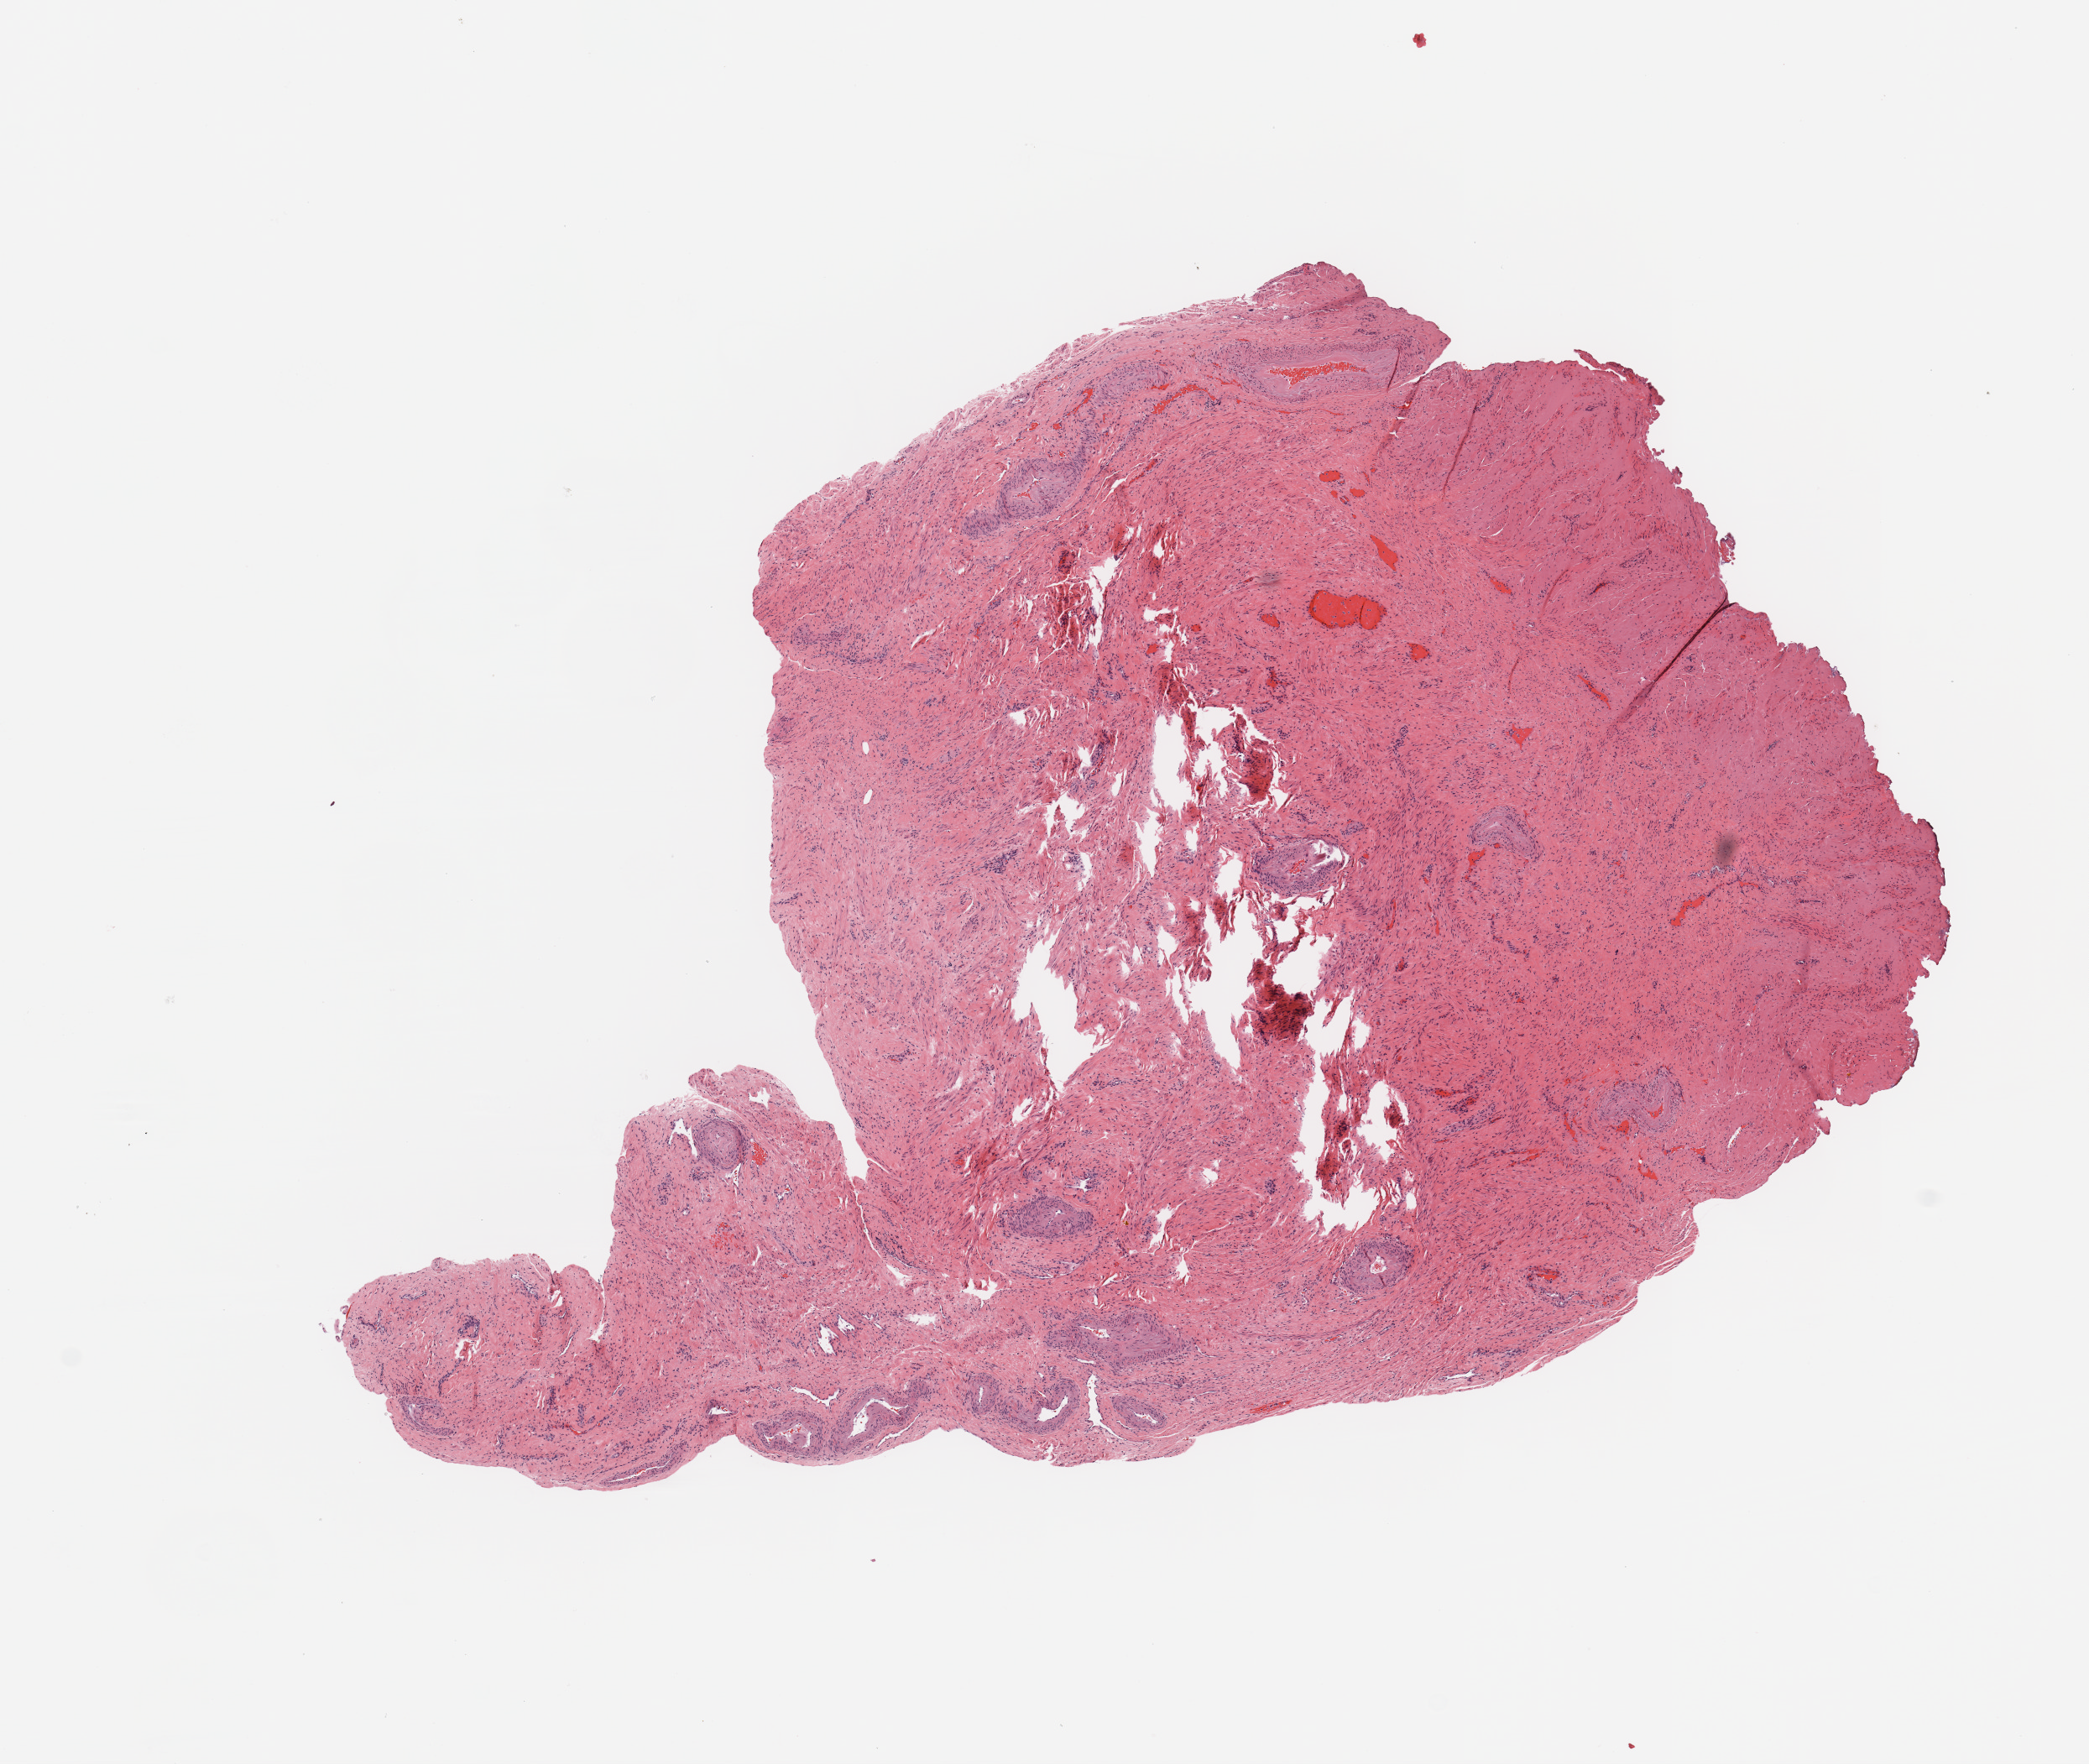
Hematoxylin and eosin (H&E) stained whole-slide image — shown as a low-resolution overview of the whole scanned area (about 9.8 x 8.3 mm, from a 20x scan). Uterus, normal (non-tumour) tissue. Female, 67 y/o.
* this section: normal (non-tumour) tissue from the same patient
* patient diagnosis: Endometrioid adenocarcinoma, NOS